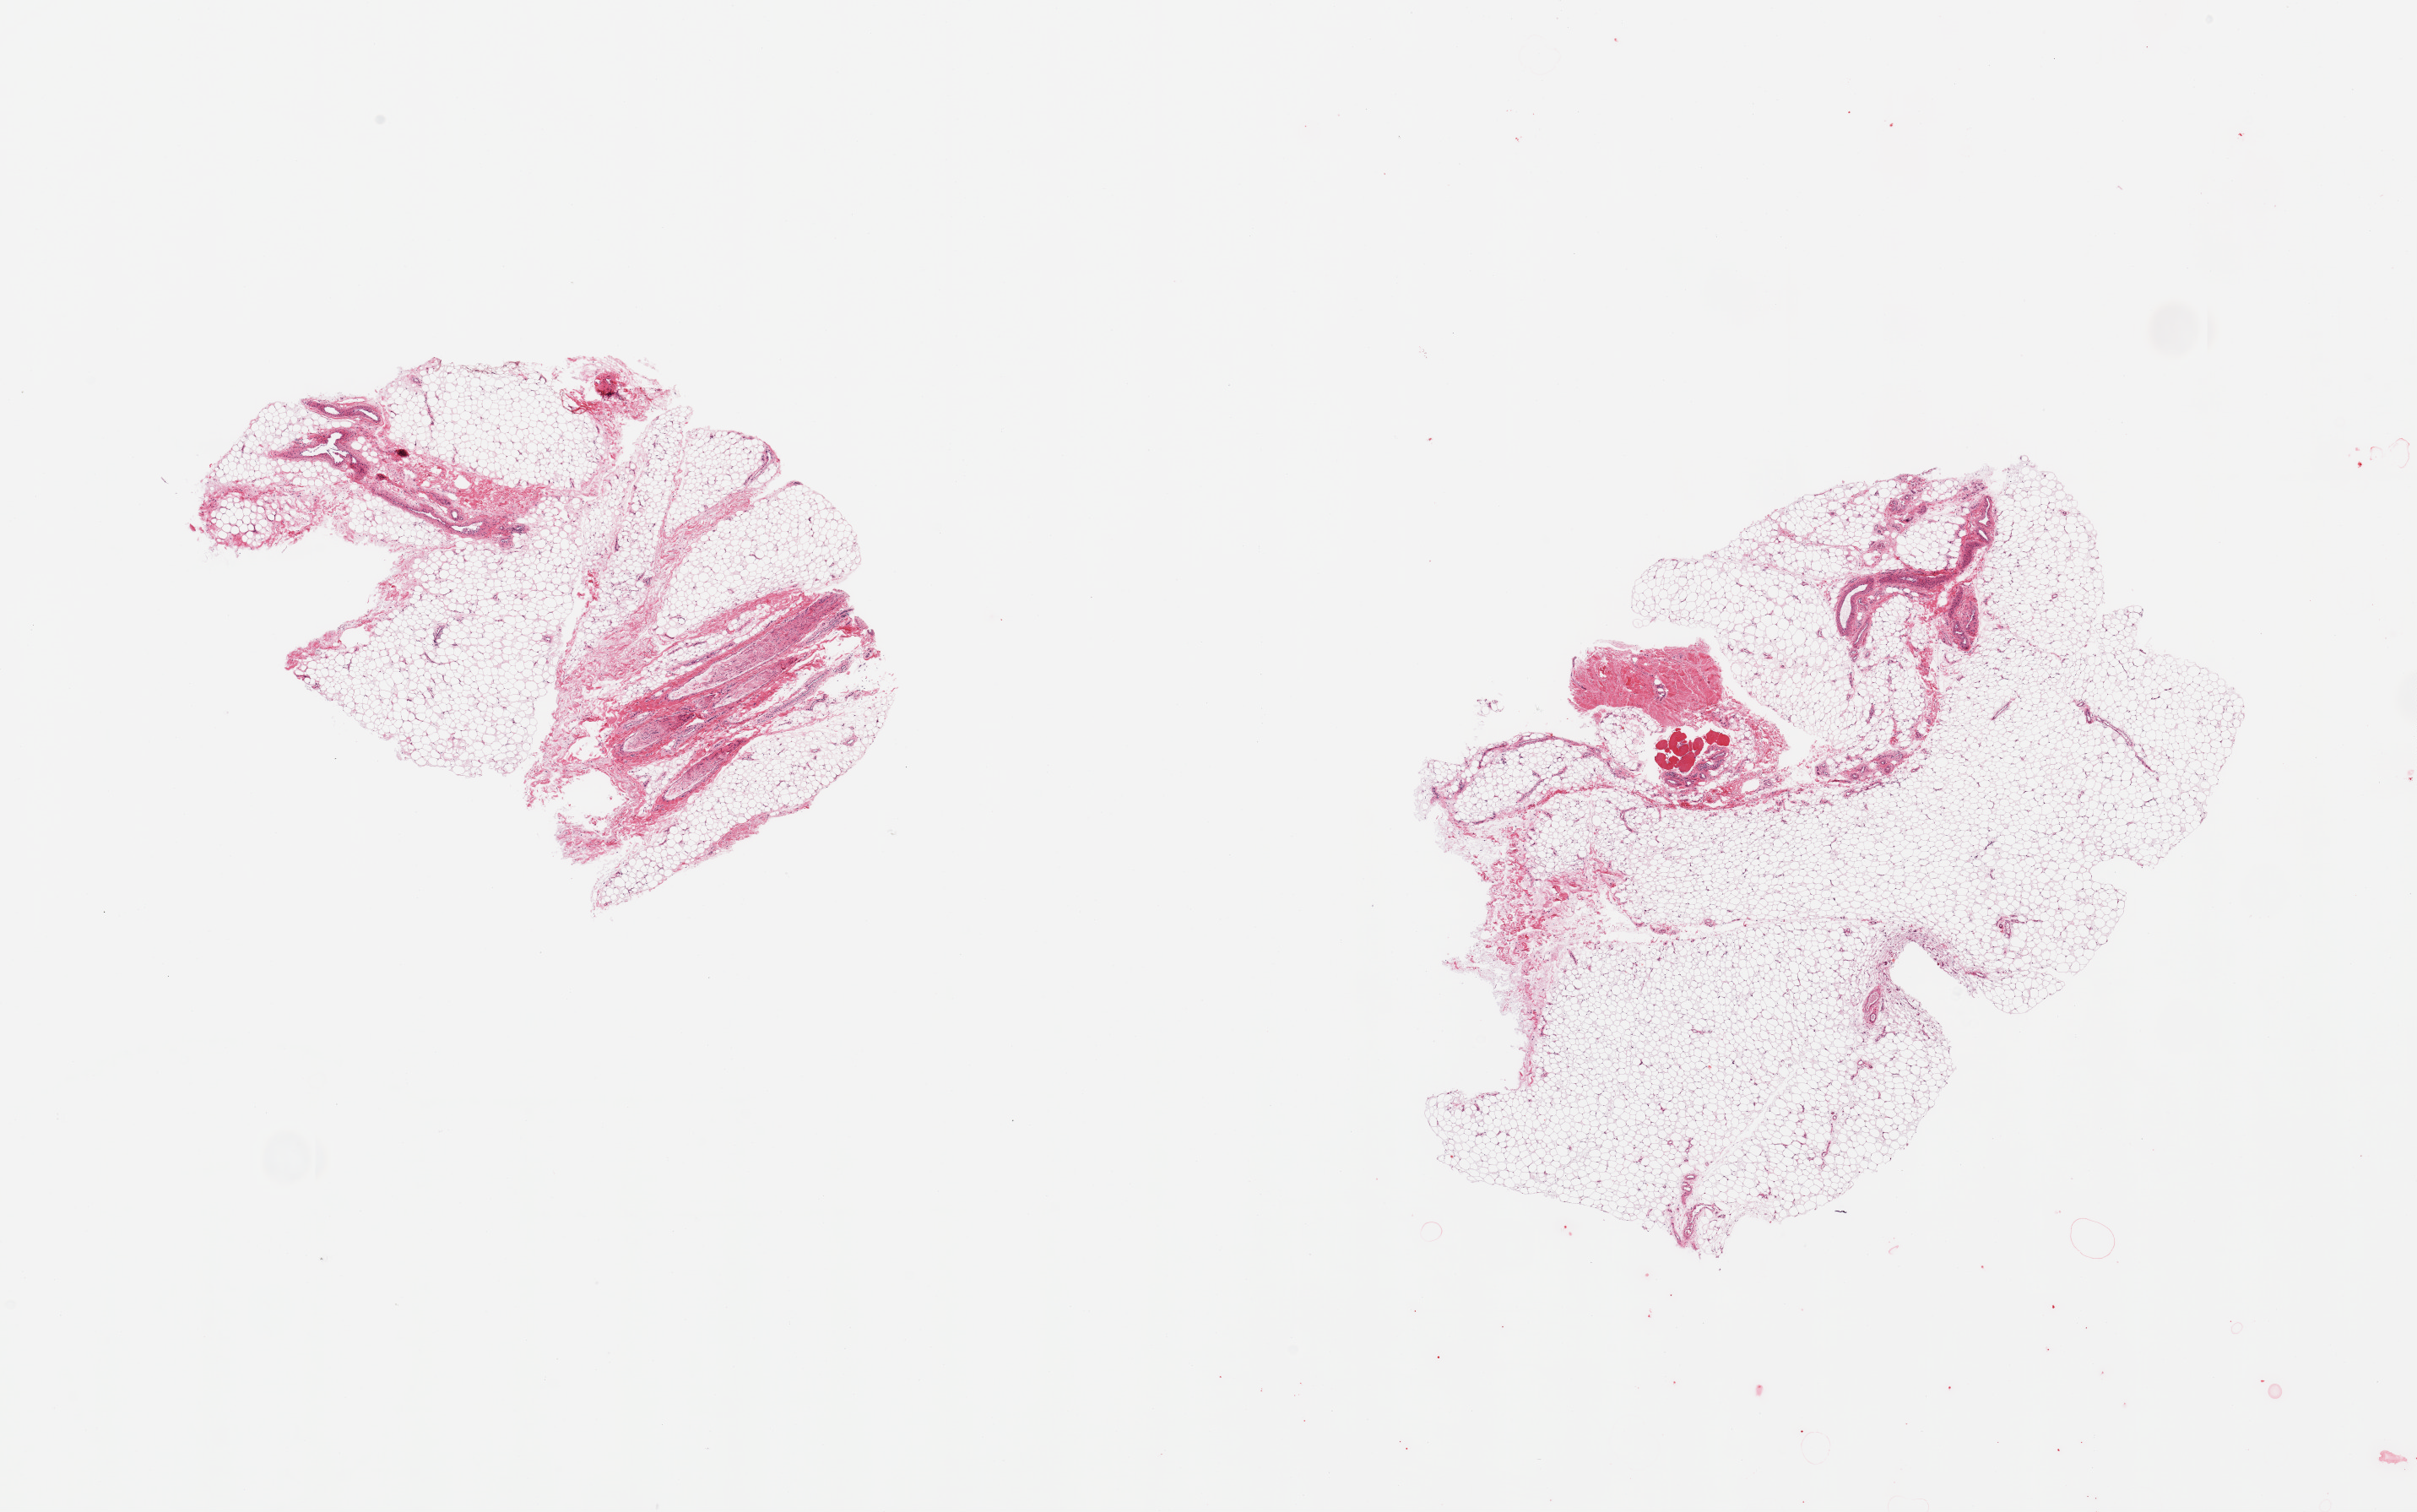
Whole-slide image, hematoxylin and eosin (H&E) stain — shown as a low-resolution overview of the whole scanned area (about 22.6 x 14.2 mm, slide scanned at 20x). PAXgene-fixed paraffin-embedded (PFPE) section. Sampled site (target tissue): adipose tissue. Donor tissue sample. Donor: male.
* review note (as recorded): 2 pieces; mature adipose tissue and ~5 and 20% fibrovascular component and nerves; small fragment of skeletal muscle